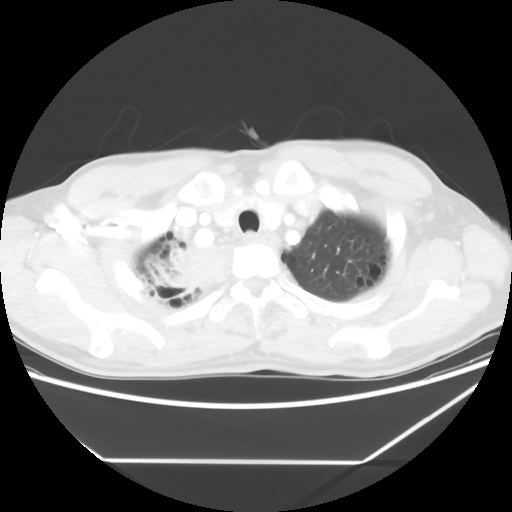
Chest CT, one axial slice; reconstruction kernel STANDARD; 120 kVp; lung window (W 1500 / L -600 HU); 5 mm slice thickness; 512 × 512 image matrix, field of view 367 × 367 mm. Patient: male, 58 years. From the clinical record (not read from this slice): clinical TNM (as recorded): T2 N2 M0.
Structures marked on this image (bounding box drawn by a radiologist):
- lung tumour (recorded histology: squamous cell carcinoma): bounding box [x1, y1, x2, y2] px = [163, 250, 231, 299]